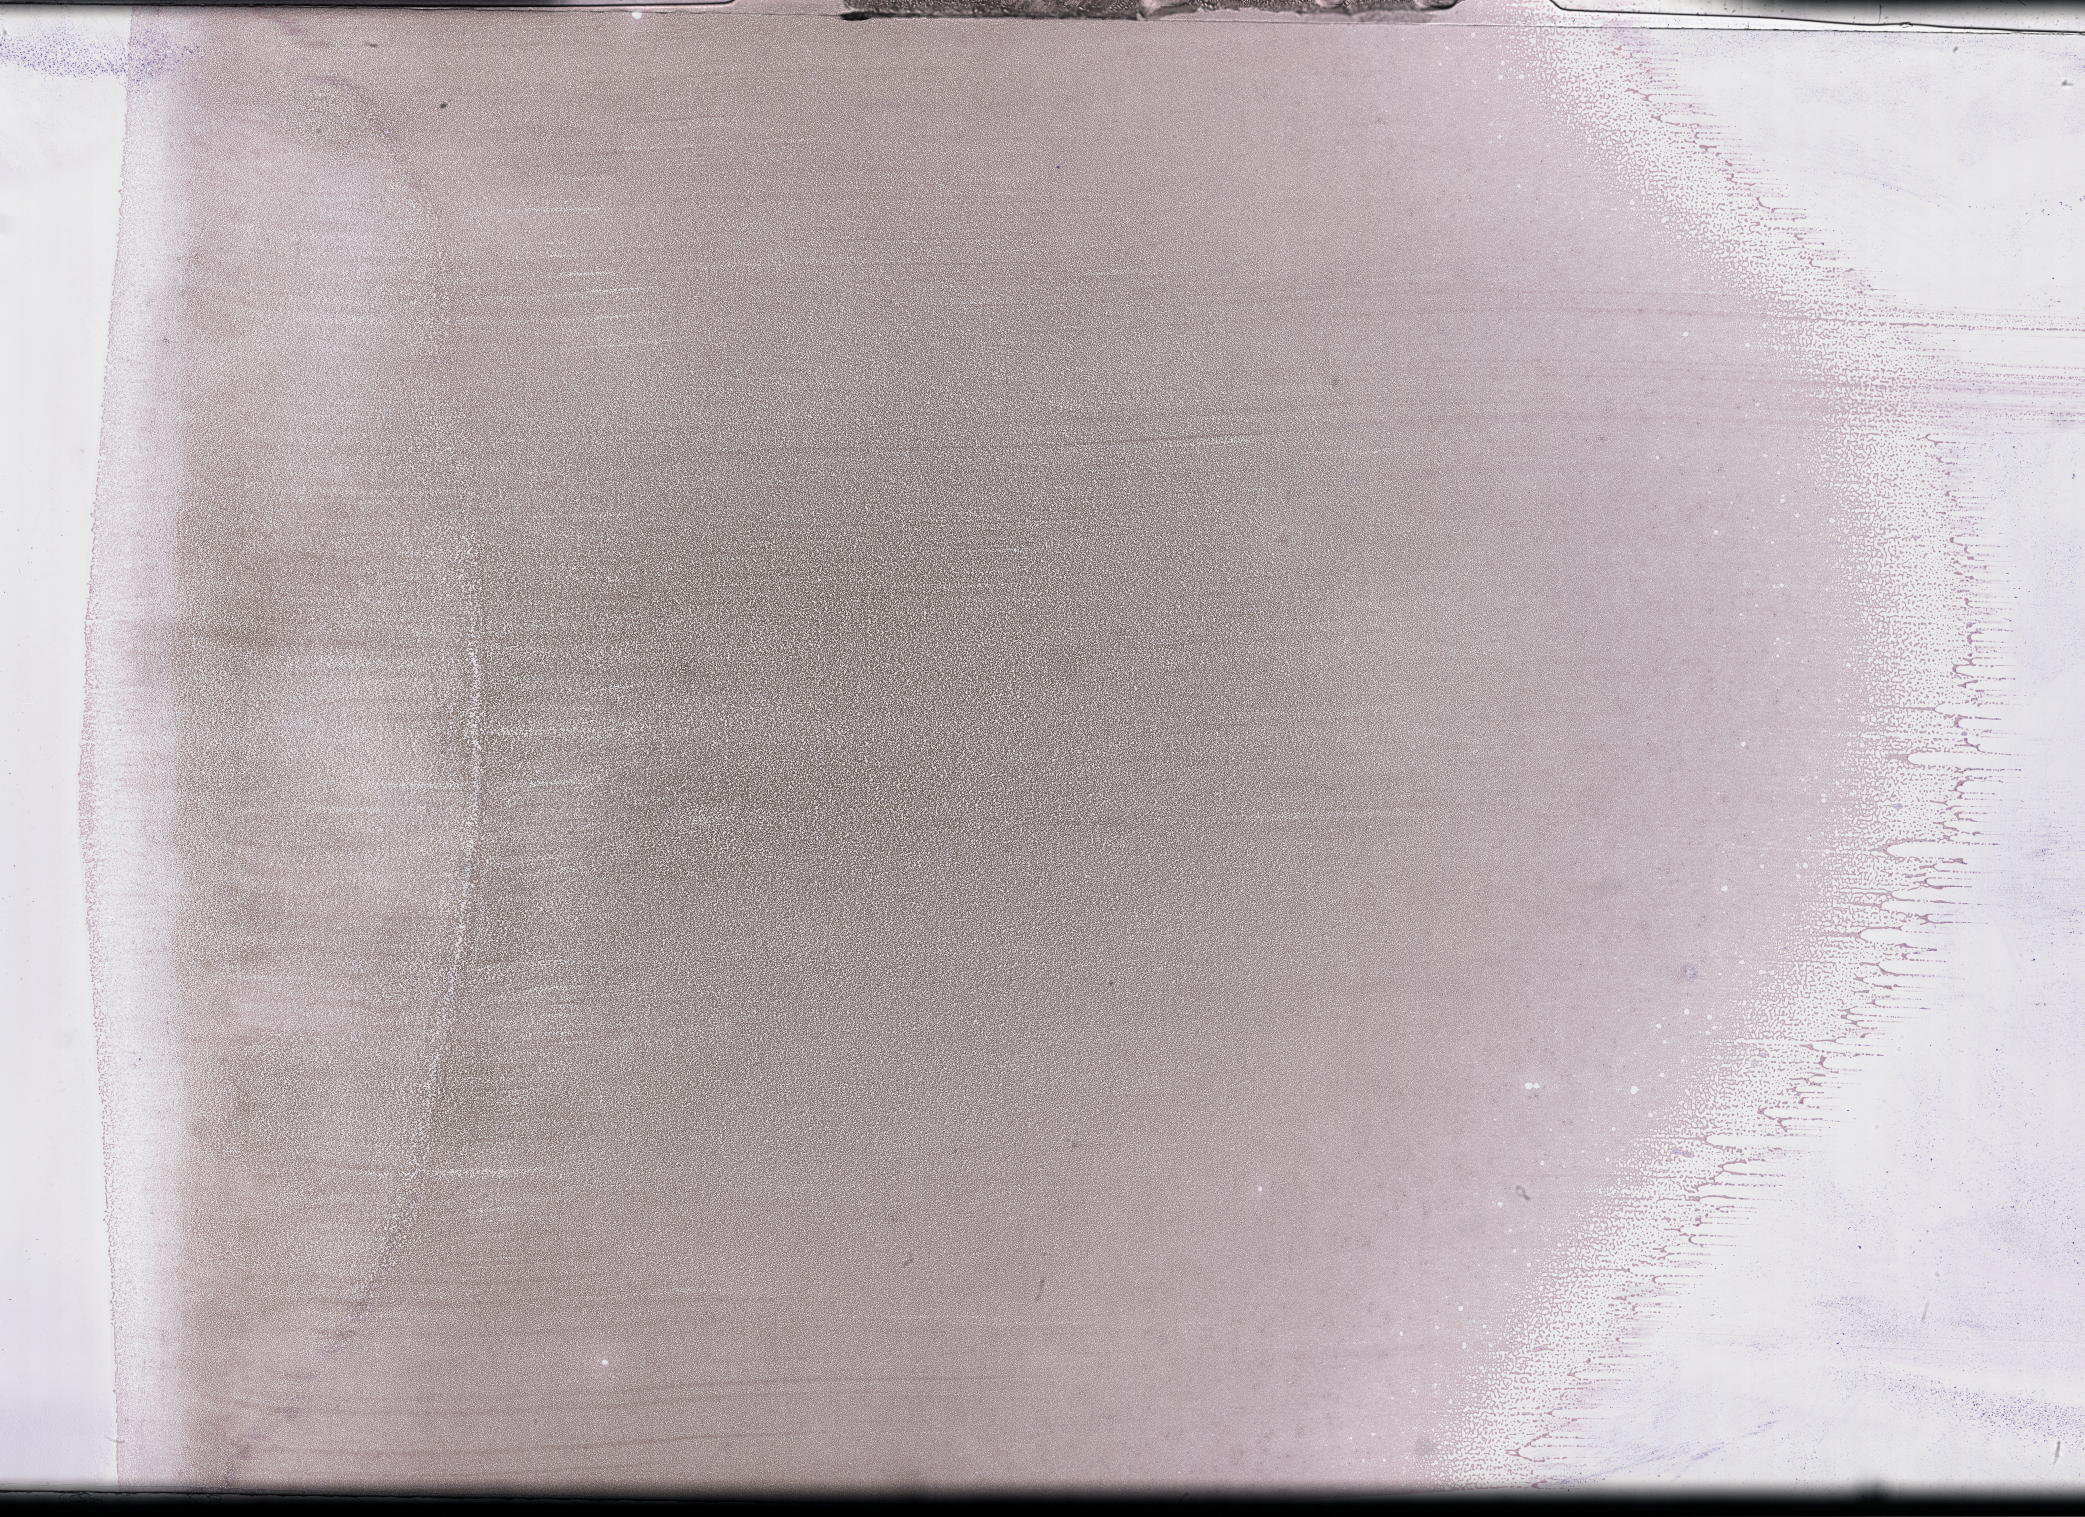
Whole-slide image of a whole blood smear, Wright–Giemsa stain, low-resolution overview of the scanned area, about 33.7 x 24.5 mm, smear from an EDTA sample, collected on treatment. Female patient.
• patient diagnosis: Plasma Cell Myeloma